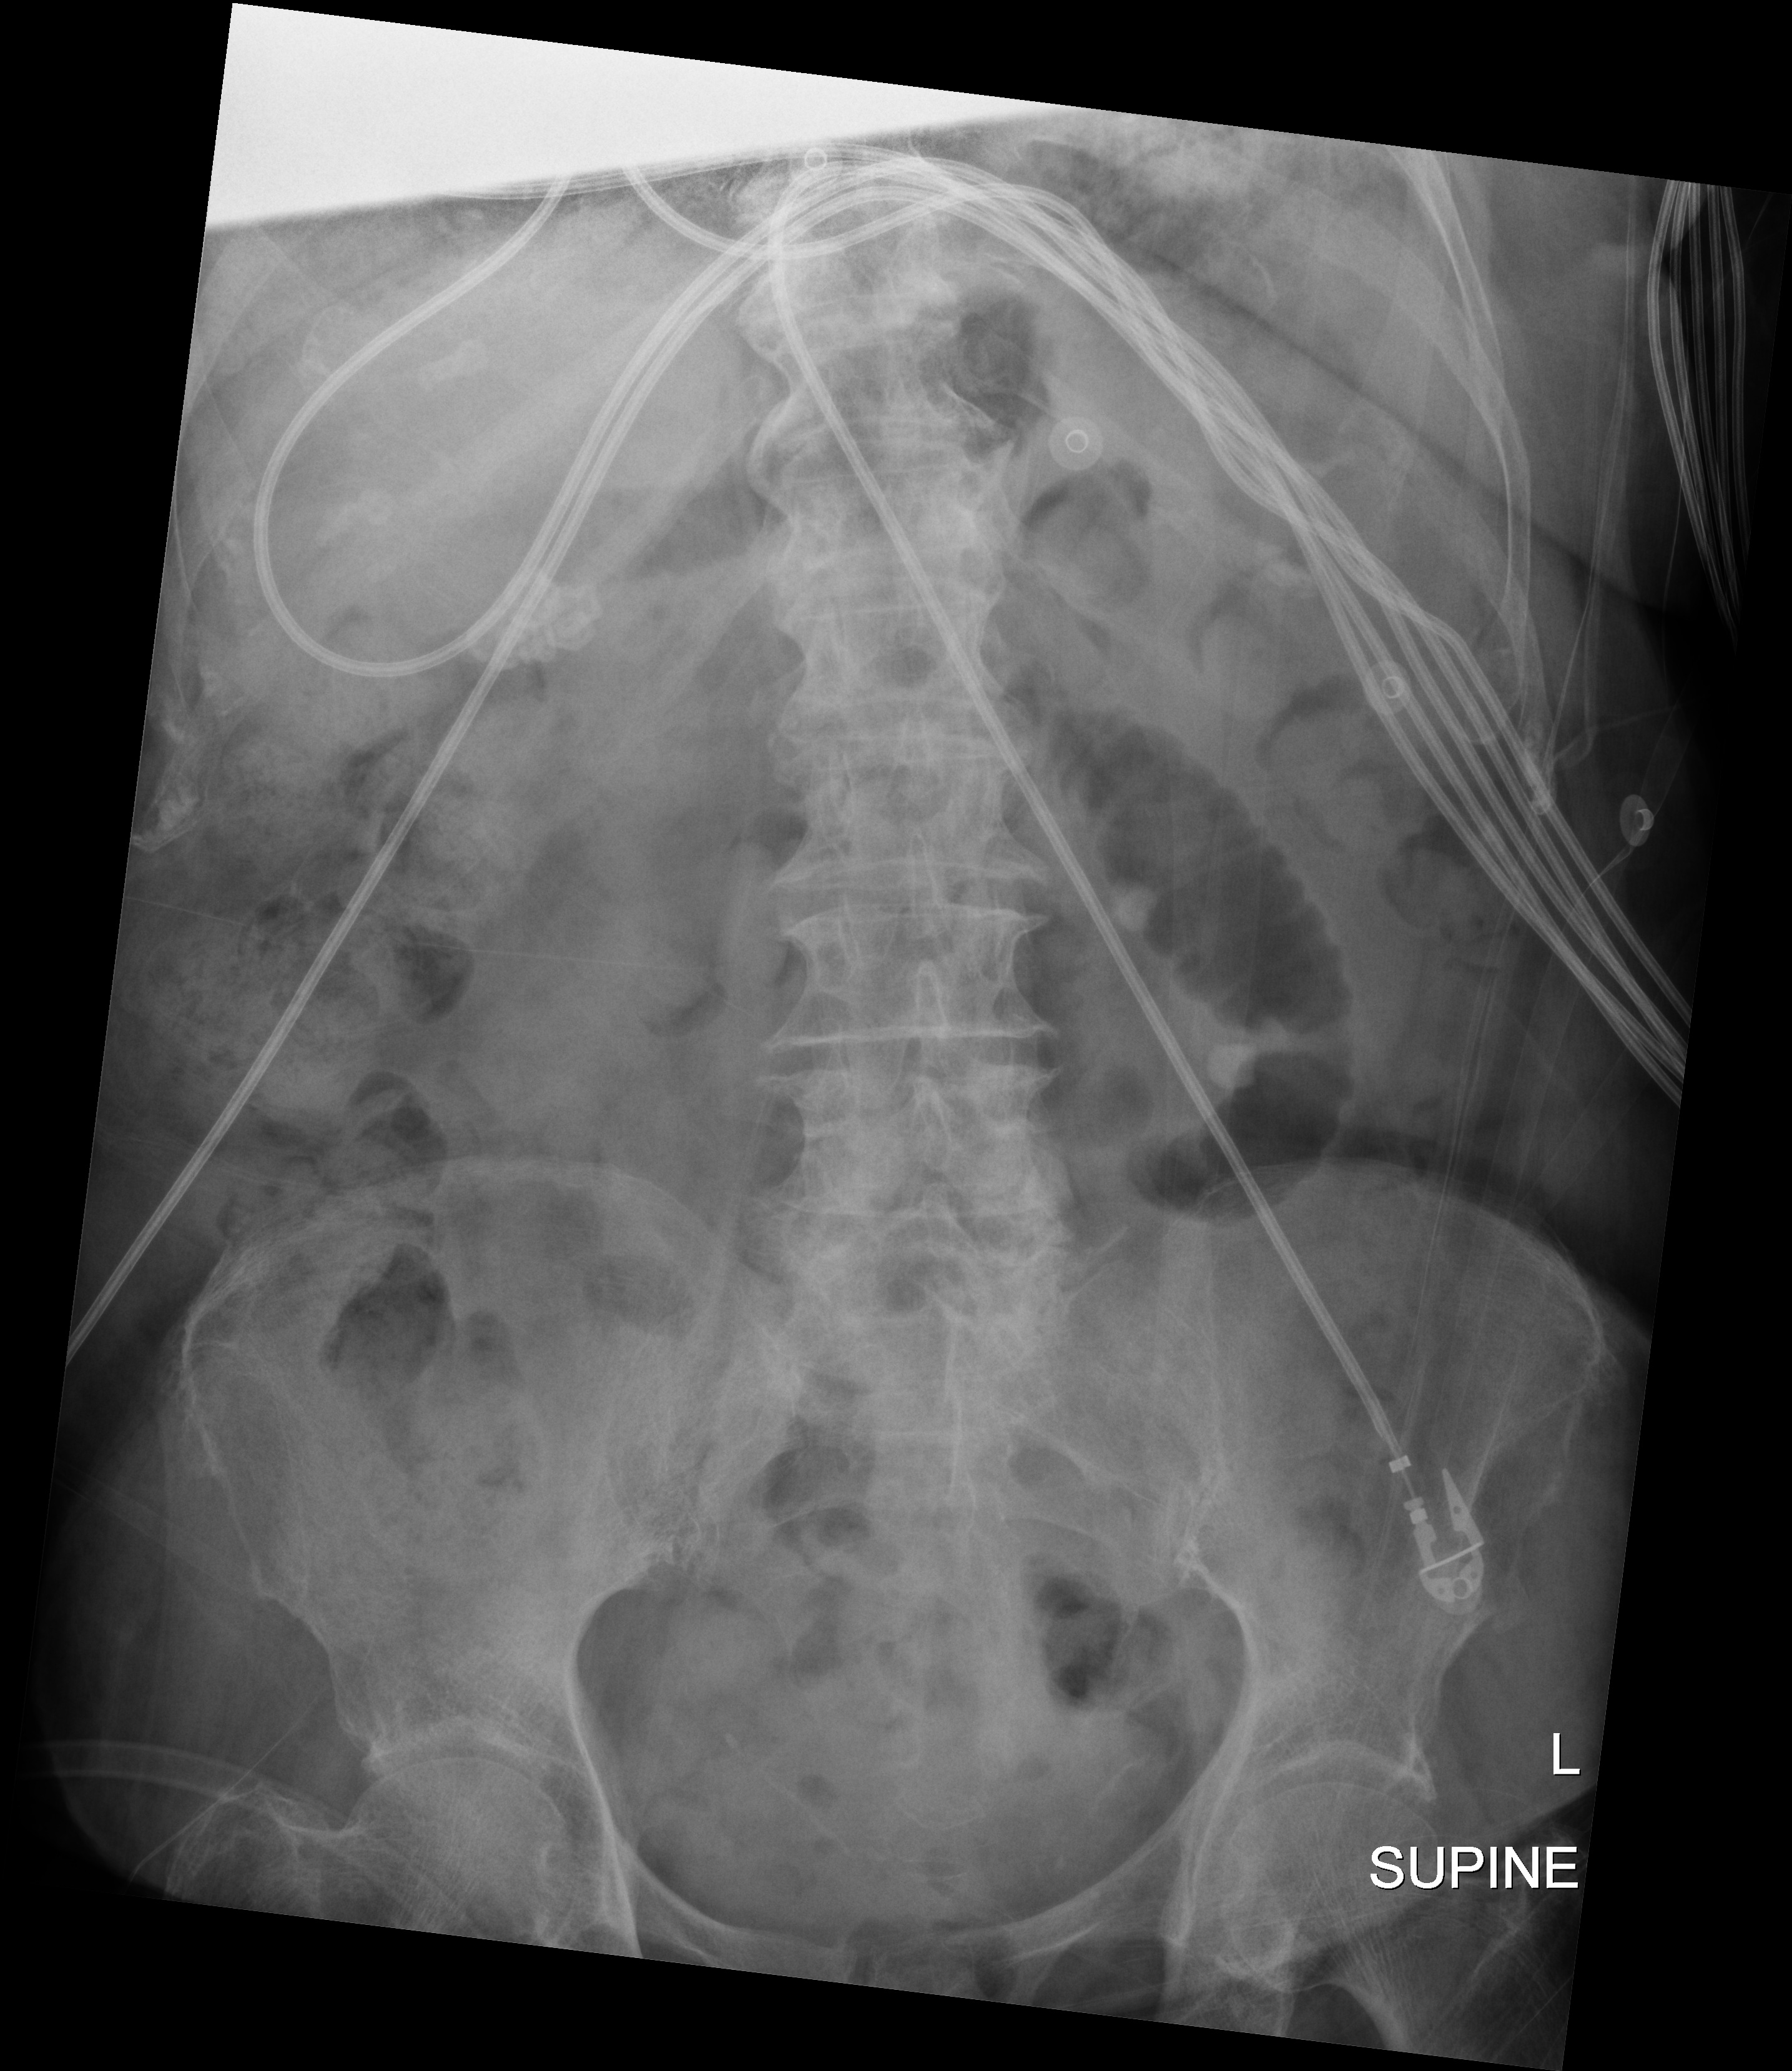
Bedside abdomen radiograph (digital radiography), anteroposterior (AP) projection. Female patient hospitalised with COVID-19, age 75–90 years.
Hospital-stay facts (about this admission, not read from this image; timing relative to this image not recorded):
- admitted to intensive care during this hospital stay: no